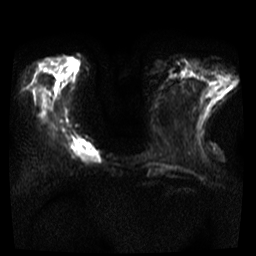
Breast MRI, one axial slice; slice 10 of 35 in the series (ordered by position); diffusion-weighted series; image 2 of 4 stored at this slice position (different b-values; order by instance number); 3 T; 5 mm slice thickness; 256 × 256 image matrix. Female patient.
Structures marked on this image (outlined manually by an expert reader):
- tumour on diffusion-weighted imaging: bounding box <69,139,101,163> (left, top, right, bottom; pixels)